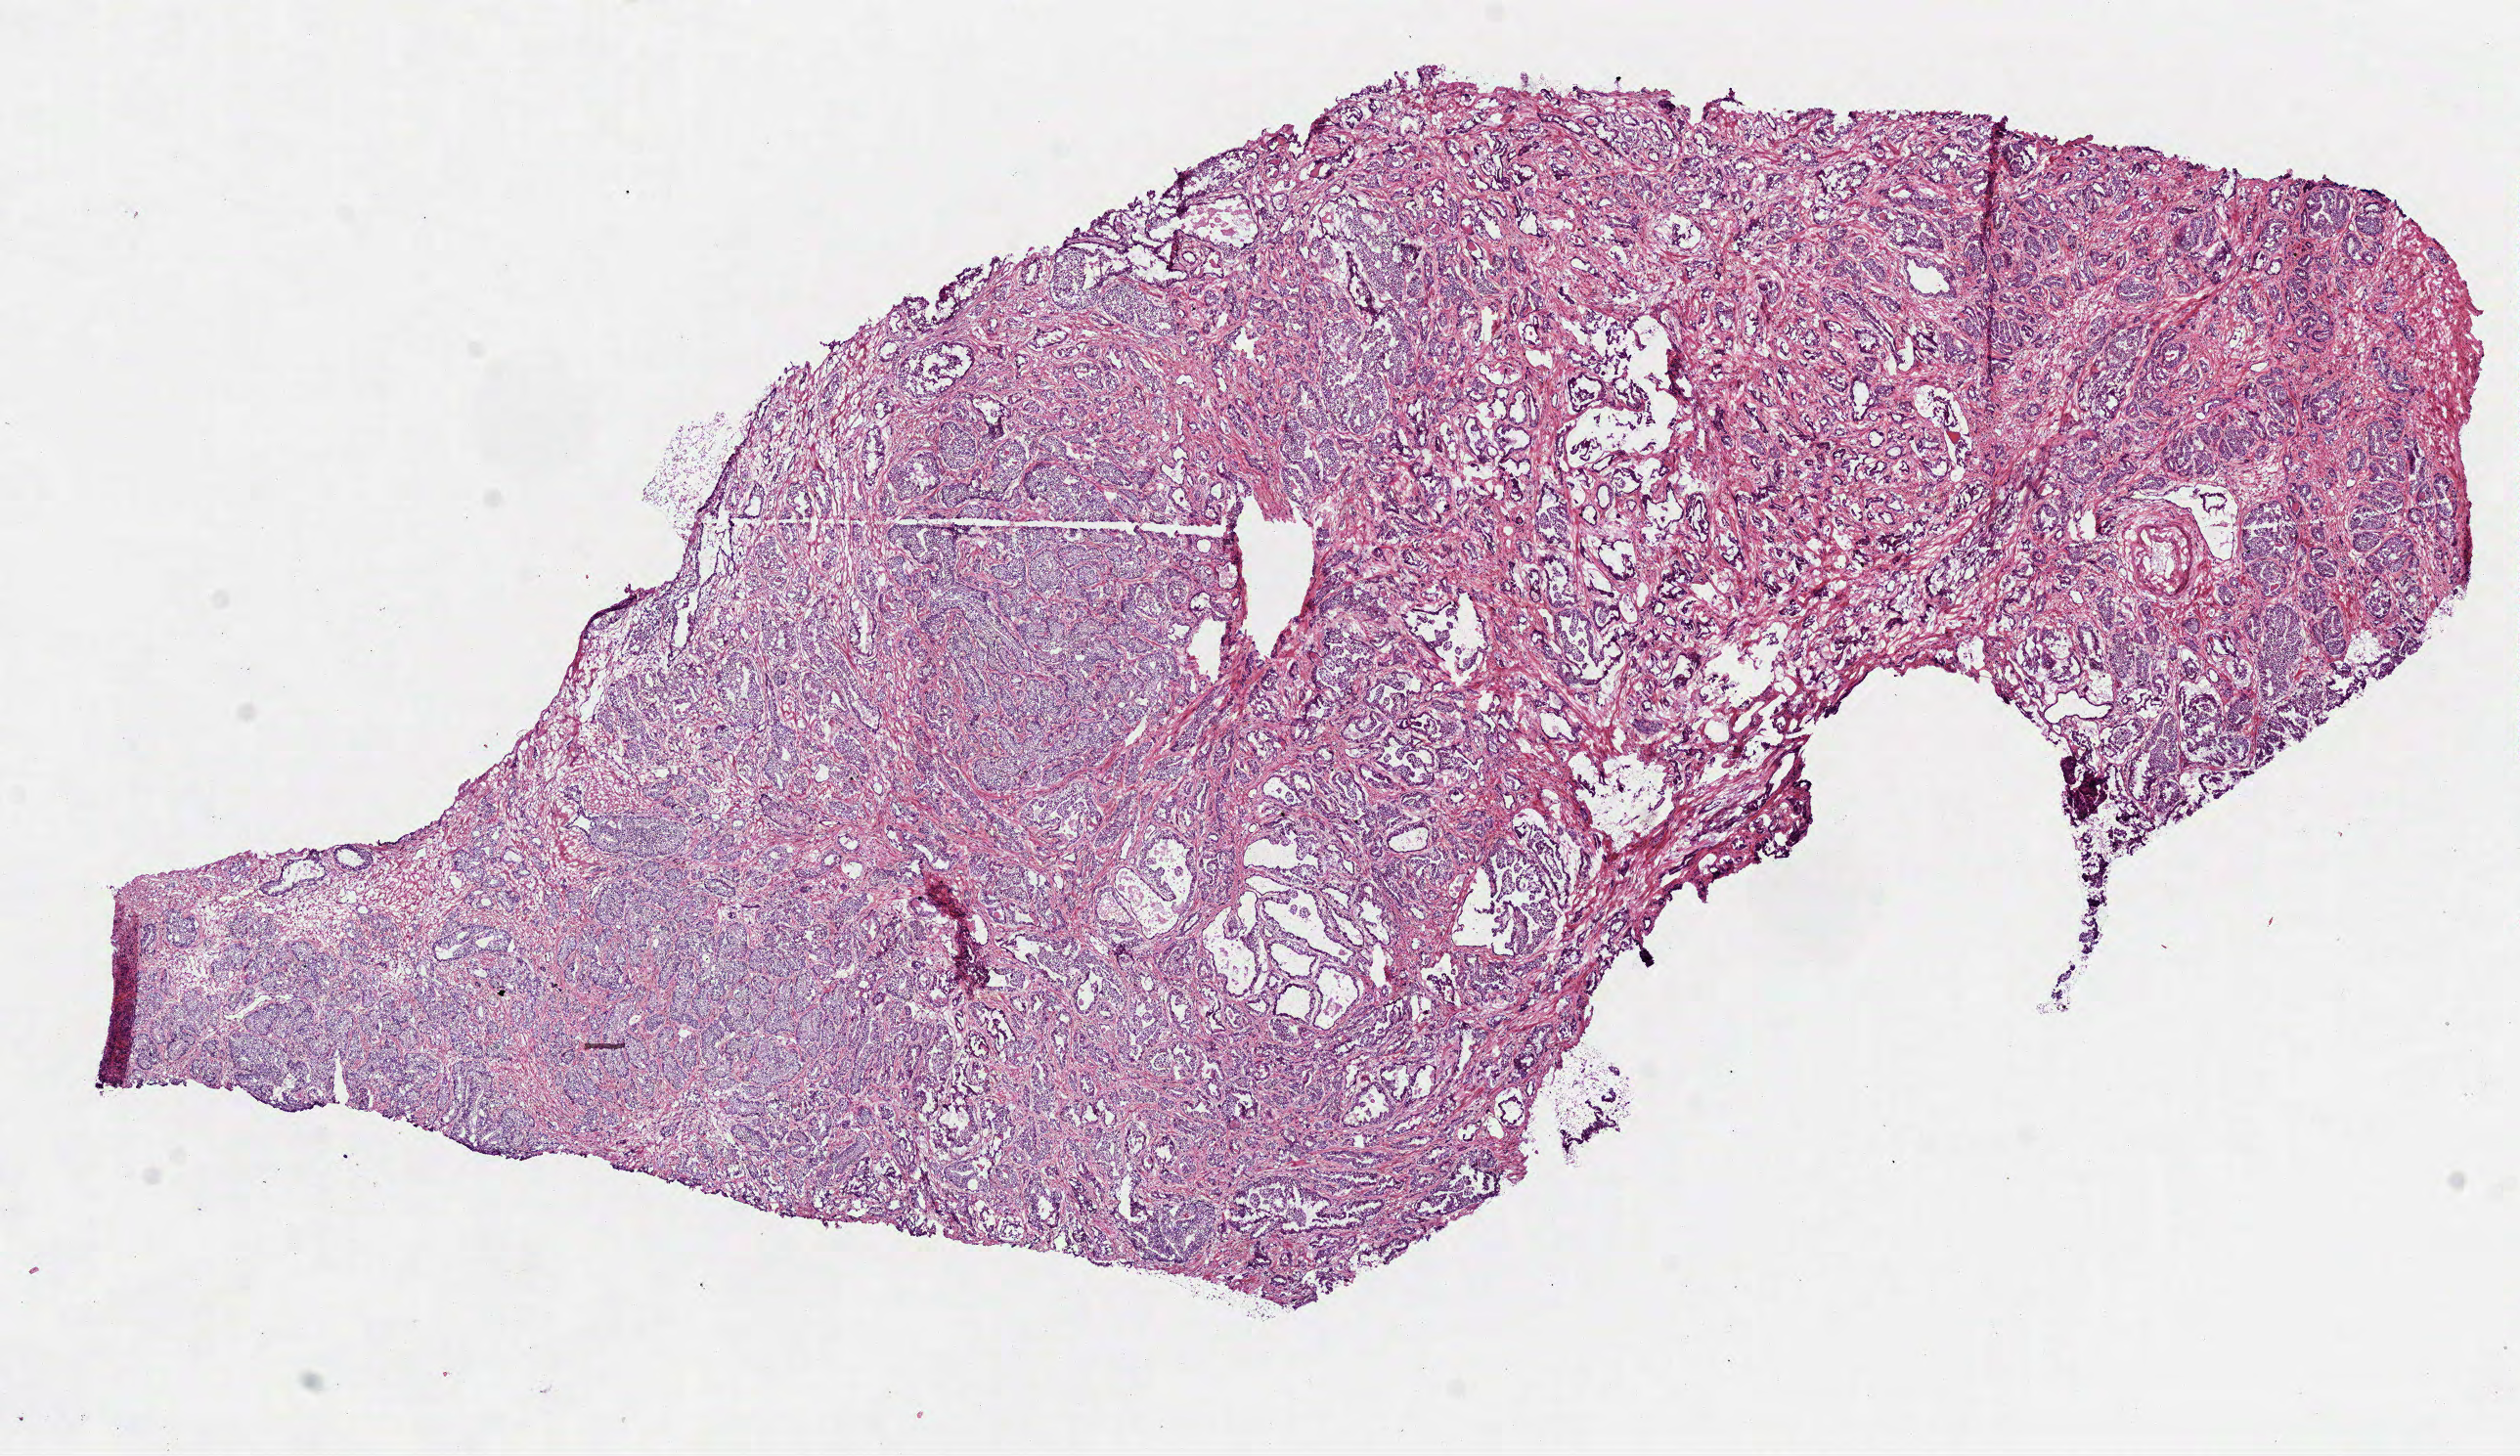
Whole-slide histology image, H&E, a low-resolution overview of the entire scanned area, about 10.4 x 6.0 mm (acquisition: 40x scan); frozen section from the top of the tissue portion; sample: primary tumour, prostate. Male patient; age at initial diagnosis 64 years. Gleason score: 6 (3+3). Slide review estimates, as recorded: tumour cells 85%, tumour nuclei 85%, normal cells 5%, stromal cells 10%, necrosis 0%.
• histologic diagnosis: Acinar cell carcinoma